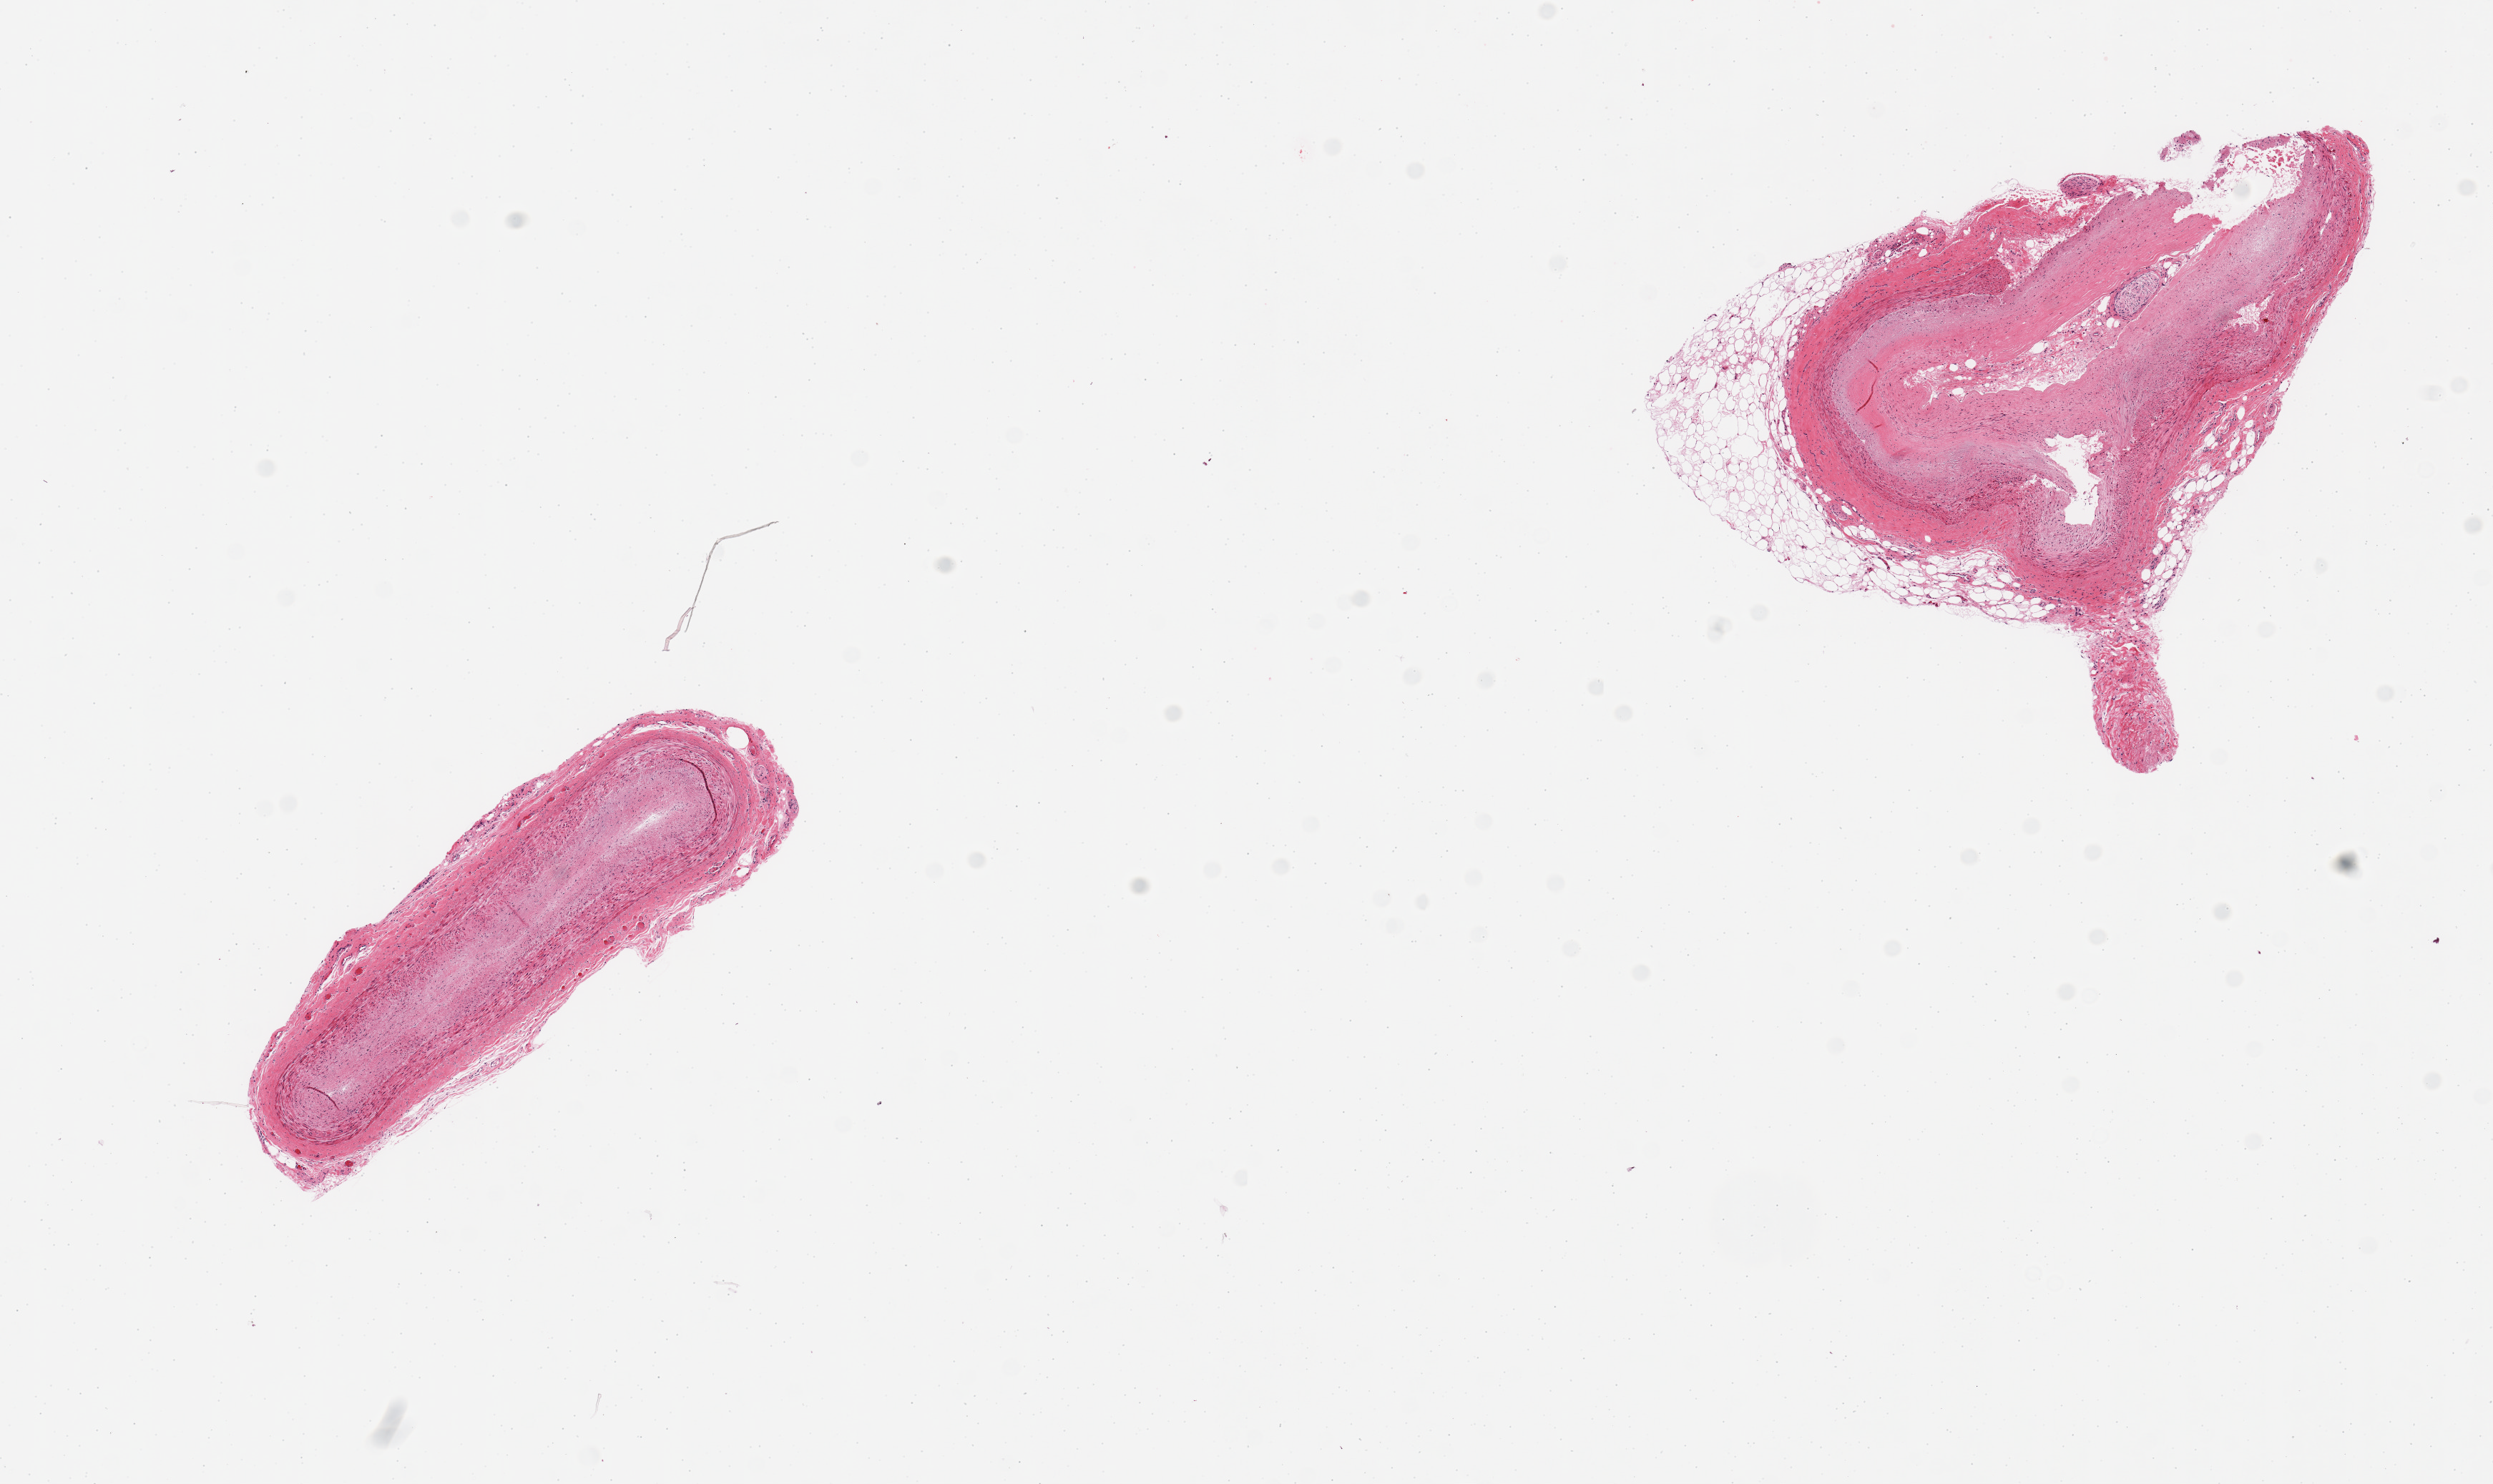
Whole-slide image, H&E stain — whole scanned area (about 13.8 x 8.2 mm) shown as a low-resolution overview, PAXgene-fixed paraffin-embedded (PFPE) section, target tissue: coronary artery, donor tissue sample. Donor sex: male.
Reviewer comment on this tissue sample: 2 pieces; moderate sclerosis; 25% fat around 1 piece.